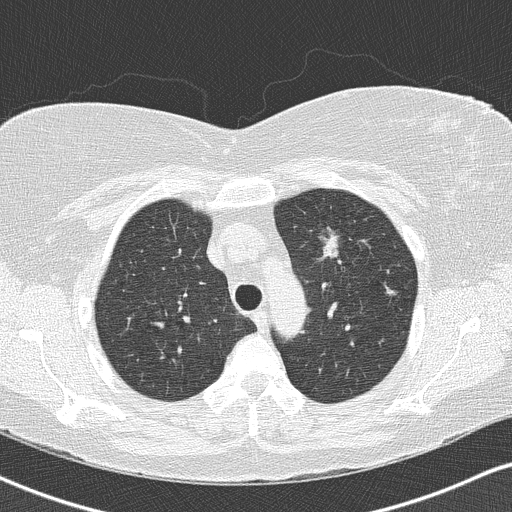
Low-dose screening chest CT, one axial slice; slice 113 of 146 in the series (ordered by position); 120 kVp; lung window (W 1500 / L -600 HU); 2 mm slice thickness; 512 × 512 image matrix, field of view 328 × 328 mm.
Structures marked on this image (expert manual segmentation):
- lesion 1 (tumor, upper lobe of left lung): bounding box [x1, y1, x2, y2] px = [319, 226, 342, 261]